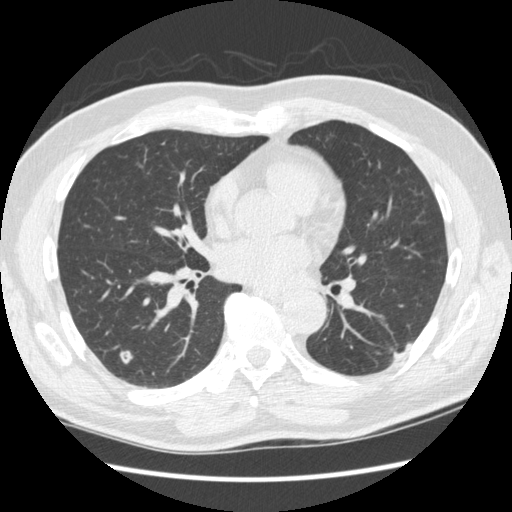
Low-dose screening chest CT, axial slice. First (baseline) screen. Lung window (W 1500 / L -600 HU). 1.25 mm slice thickness. Standard (soft-tissue) reconstruction kernel (STANDARD). 120 kVp. Slice 133 of 267 in the series. 512 × 512 image matrix. Male, age 74 years at enrolment.
Expert-annotated lung lesion, bounding box <376,324,419,377> (left, top, right, bottom; pixels). The screening reader recorded 3 non-calcified nodules or masses ≥4 mm on this exam (right upper lobe, right lower lobe, left upper lobe); which of them this box marks is not recorded. Participant outcome: lung cancer diagnosed 384 days after this screen — squamous cell carcinoma, NOS, left lower lobe, well differentiated (G1), stage IA (AJCC 6th edition), 28 mm at pathology.